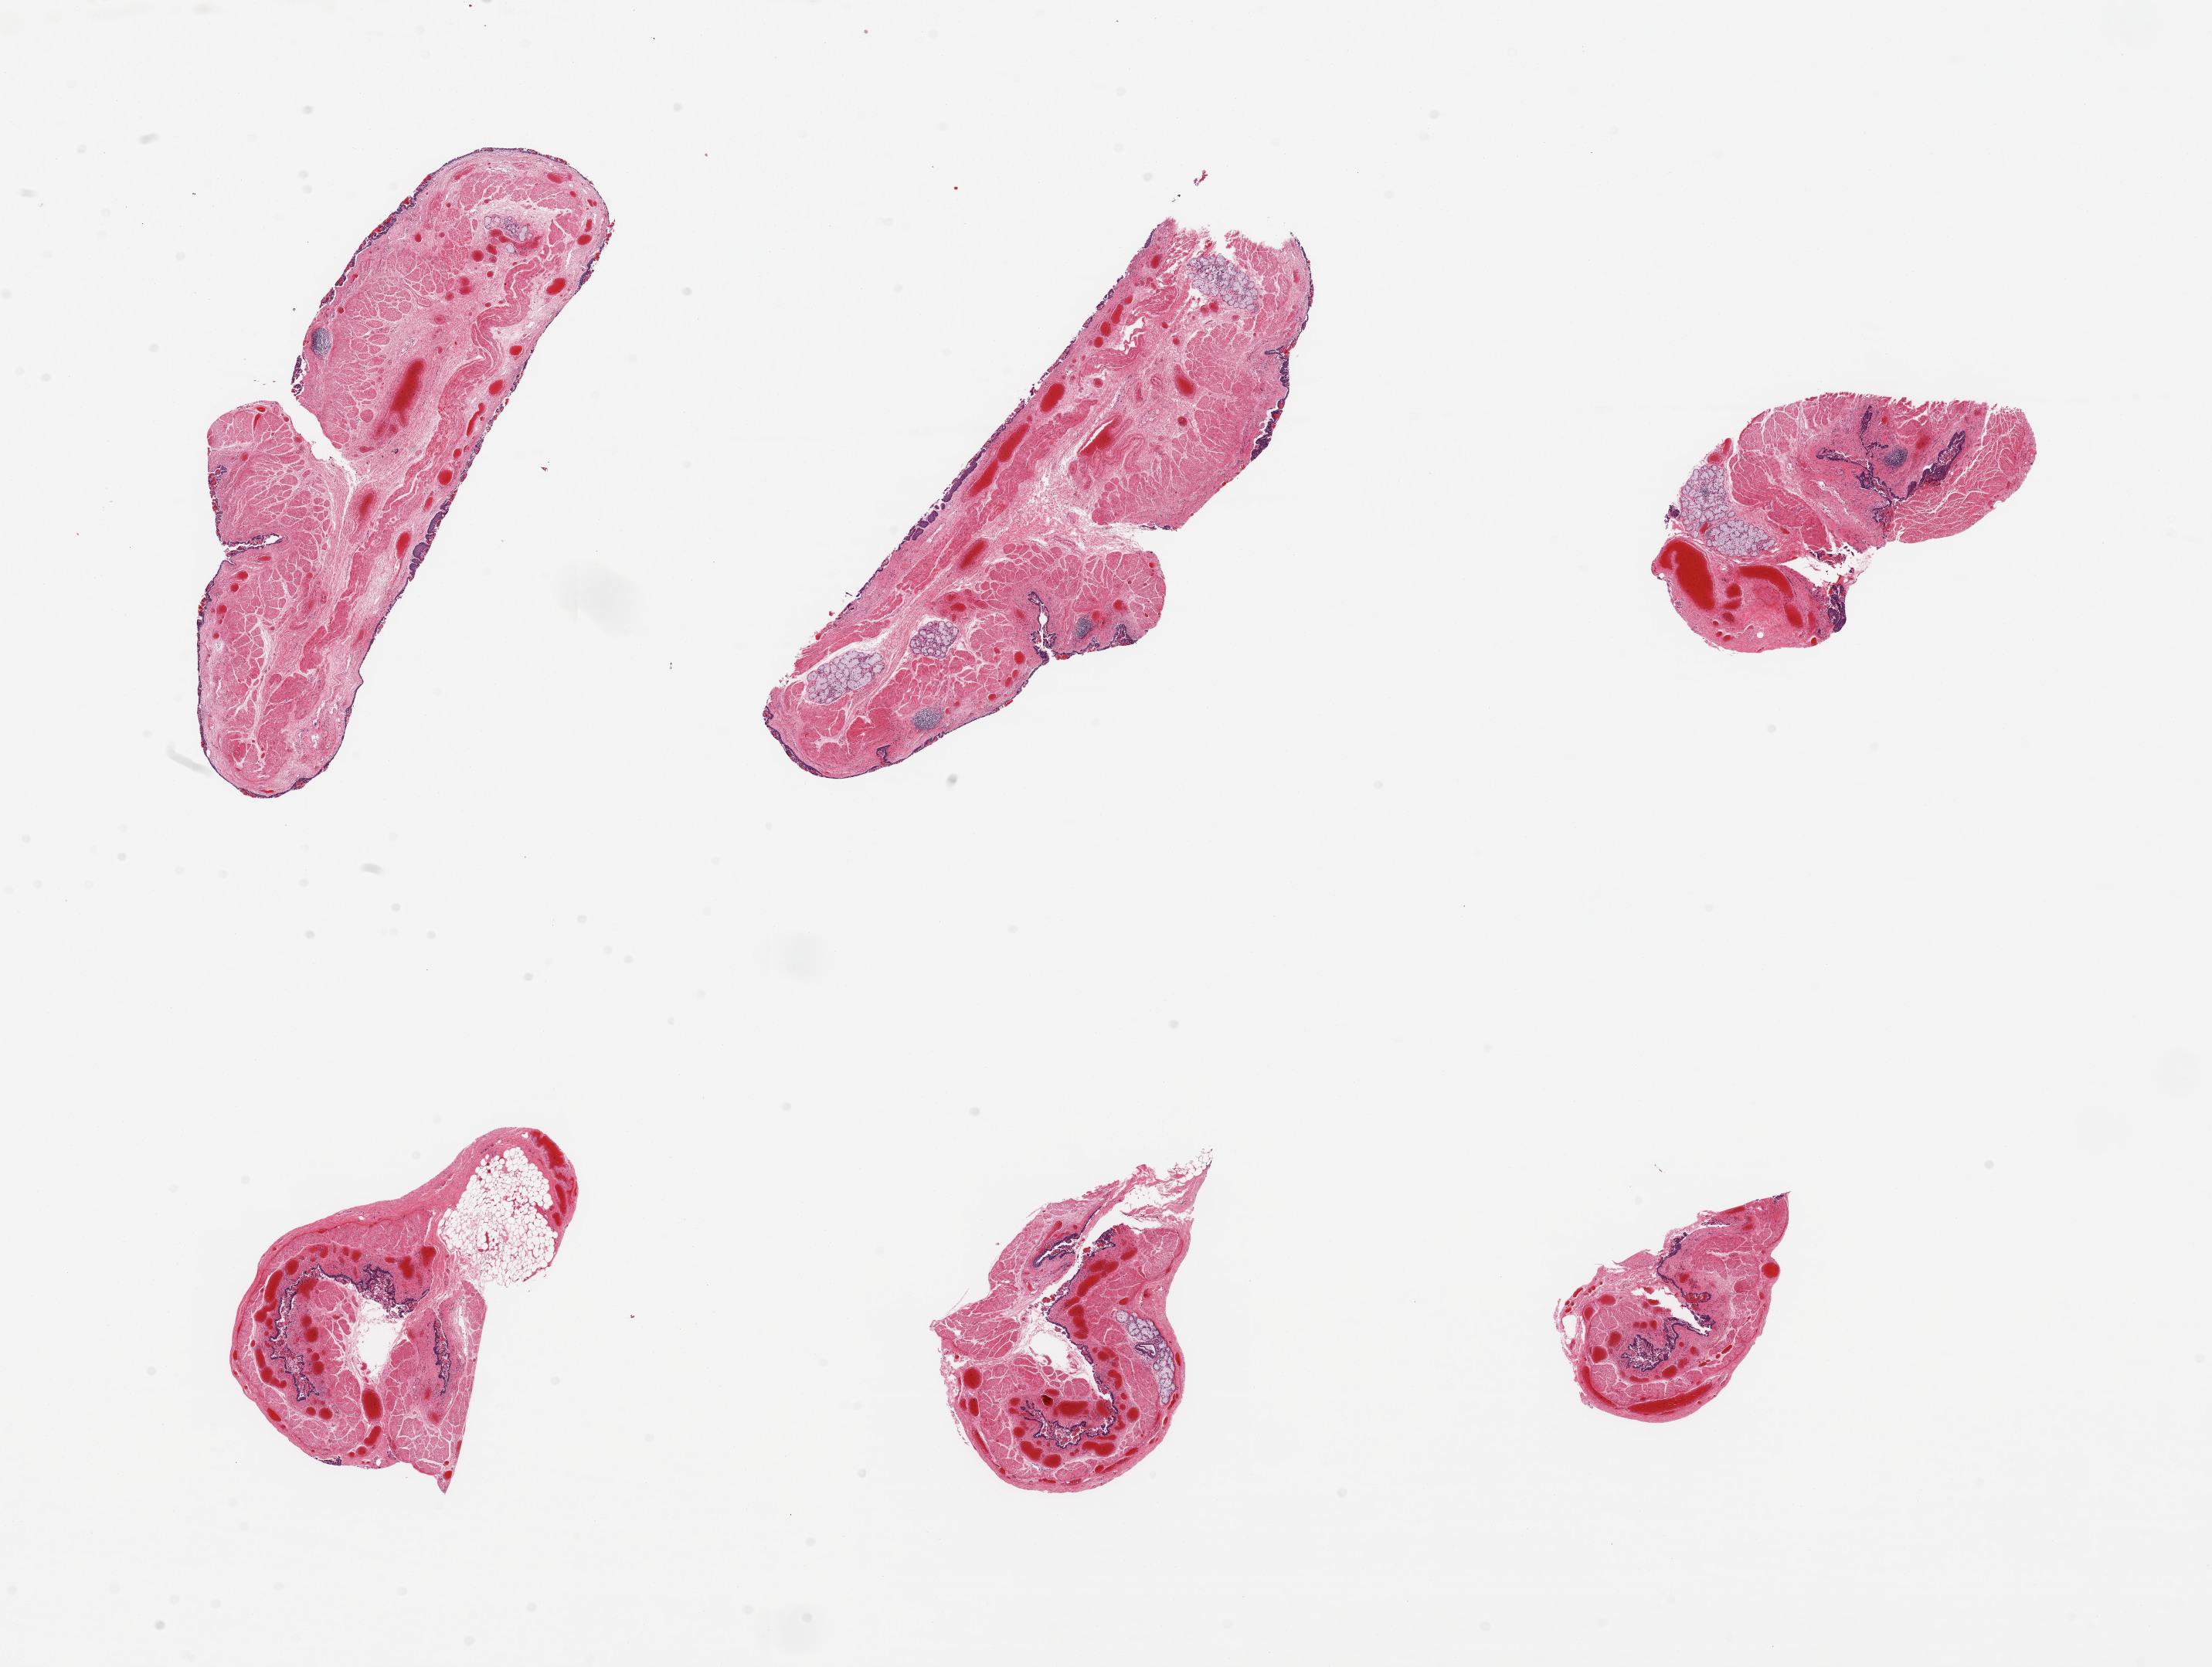
Digitized H&E-stained section, brightfield, a low-resolution overview of the entire scanned area, about 22.6 x 17.1 mm (from a 20x scan); PAXgene-fixed, paraffin-embedded tissue; target tissue: esophageal mucous membrane; donor tissue sample. Donor: male.
Review note (as recorded): 6 pieces; mucosa largely autolyzed/sloughed submucosal glands, preserved muscularis, congestion.